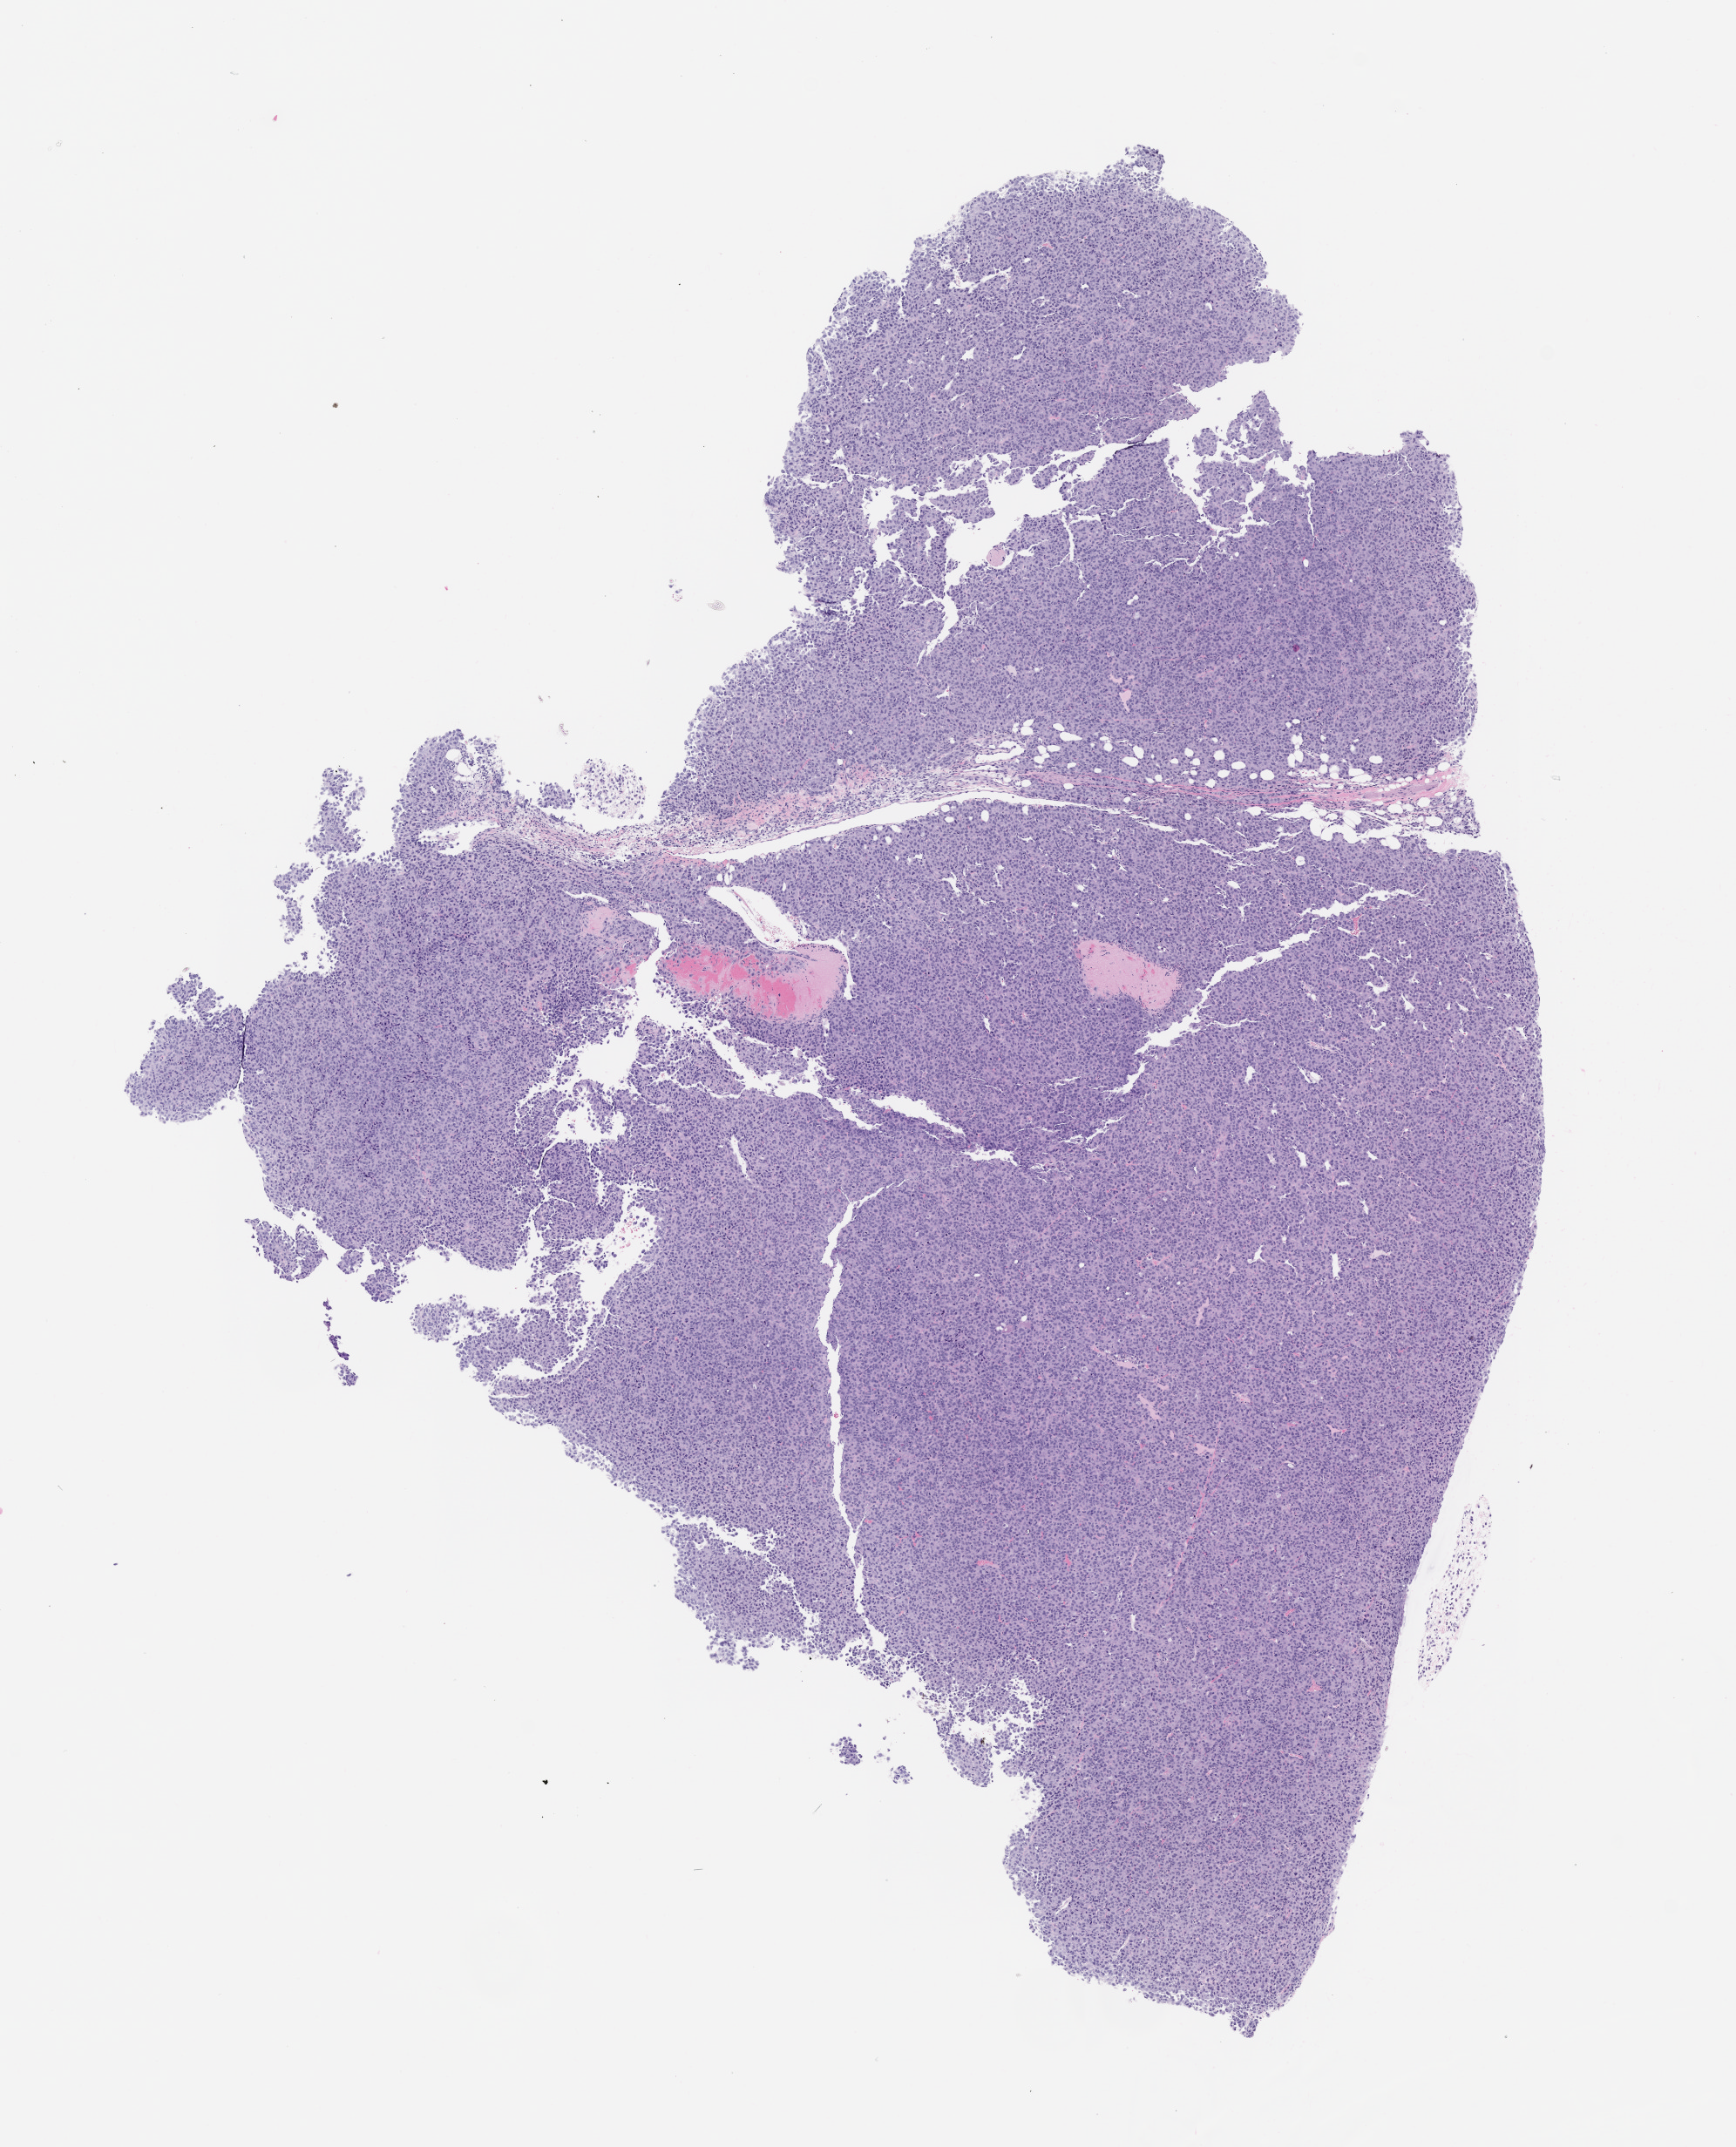
Hematoxylin and eosin (H&E) whole-slide image of a patient-derived xenograft (PDX) tumor grown in a mouse, passage 1 — low-resolution overview of the scanned area, about 8.0 x 9.9 mm. FFPE section. Originating tumor site category: bone.
* originating patient diagnosis: Osteosarcoma